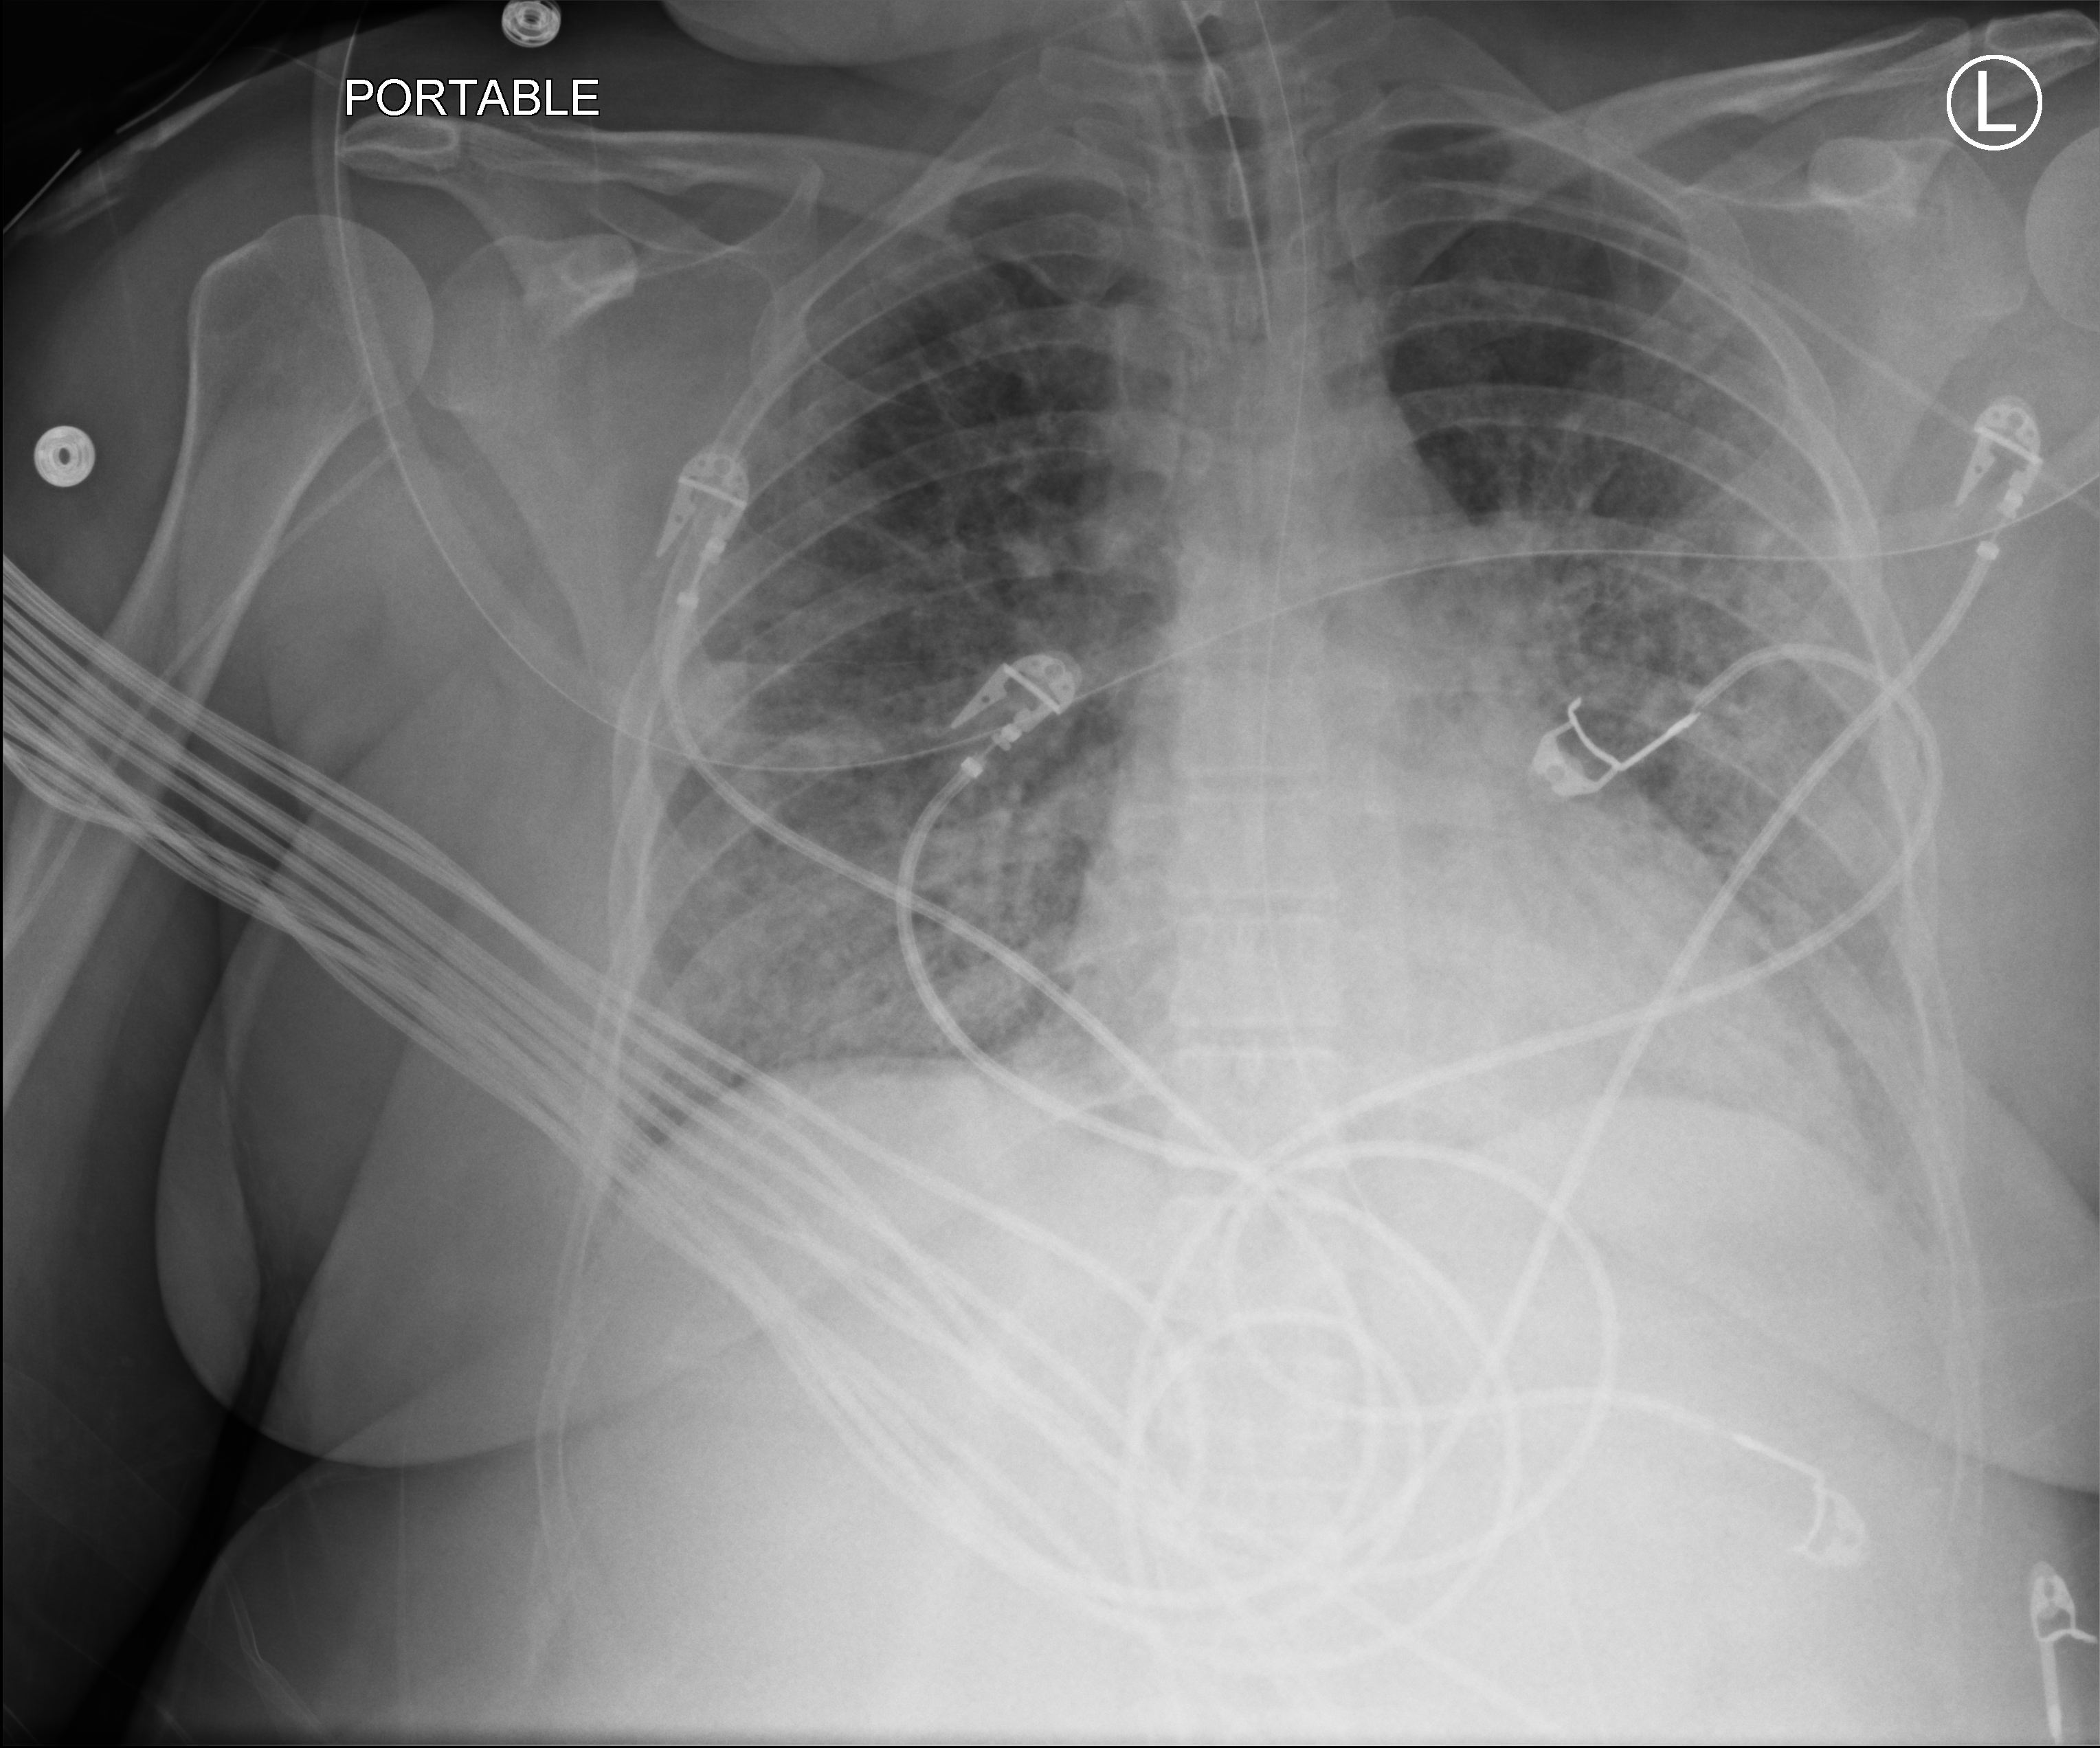
Chest X-ray (portable), anteroposterior (AP) projection. Patient hospitalised with COVID-19; female, aged 18–59 years.
Admission-level facts for this patient (not findings on this image; timing relative to this image not recorded): chronic kidney disease (admission record): no.